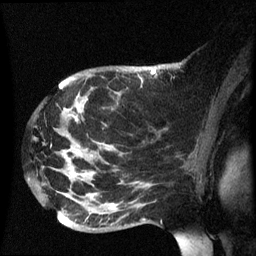
Breast MRI (dynamic contrast-enhanced), one sagittal slice; slice 43 of 60 in the series (ordered by position); dynamic contrast-enhanced series, image 2 of 3 at this slice position (ordered by acquisition); 1.5 T; TE 4.2 ms, TR 8.4 ms; 2.5 mm slice thickness; 256 × 256 image matrix. Patient: female, 49 years.
Annotated regions visible in this slice (semi-automatically segmented with operator editing):
- analysis volume of interest (the breast-tissue region the enhancement analysis was run in; not a lesion): bounding box <30,72,158,233> (left, top, right, bottom; pixels)
- tumour enhancement mask (voxels above the 70 % enhancement threshold inside the analysis volume of interest): <152,72,154,75>